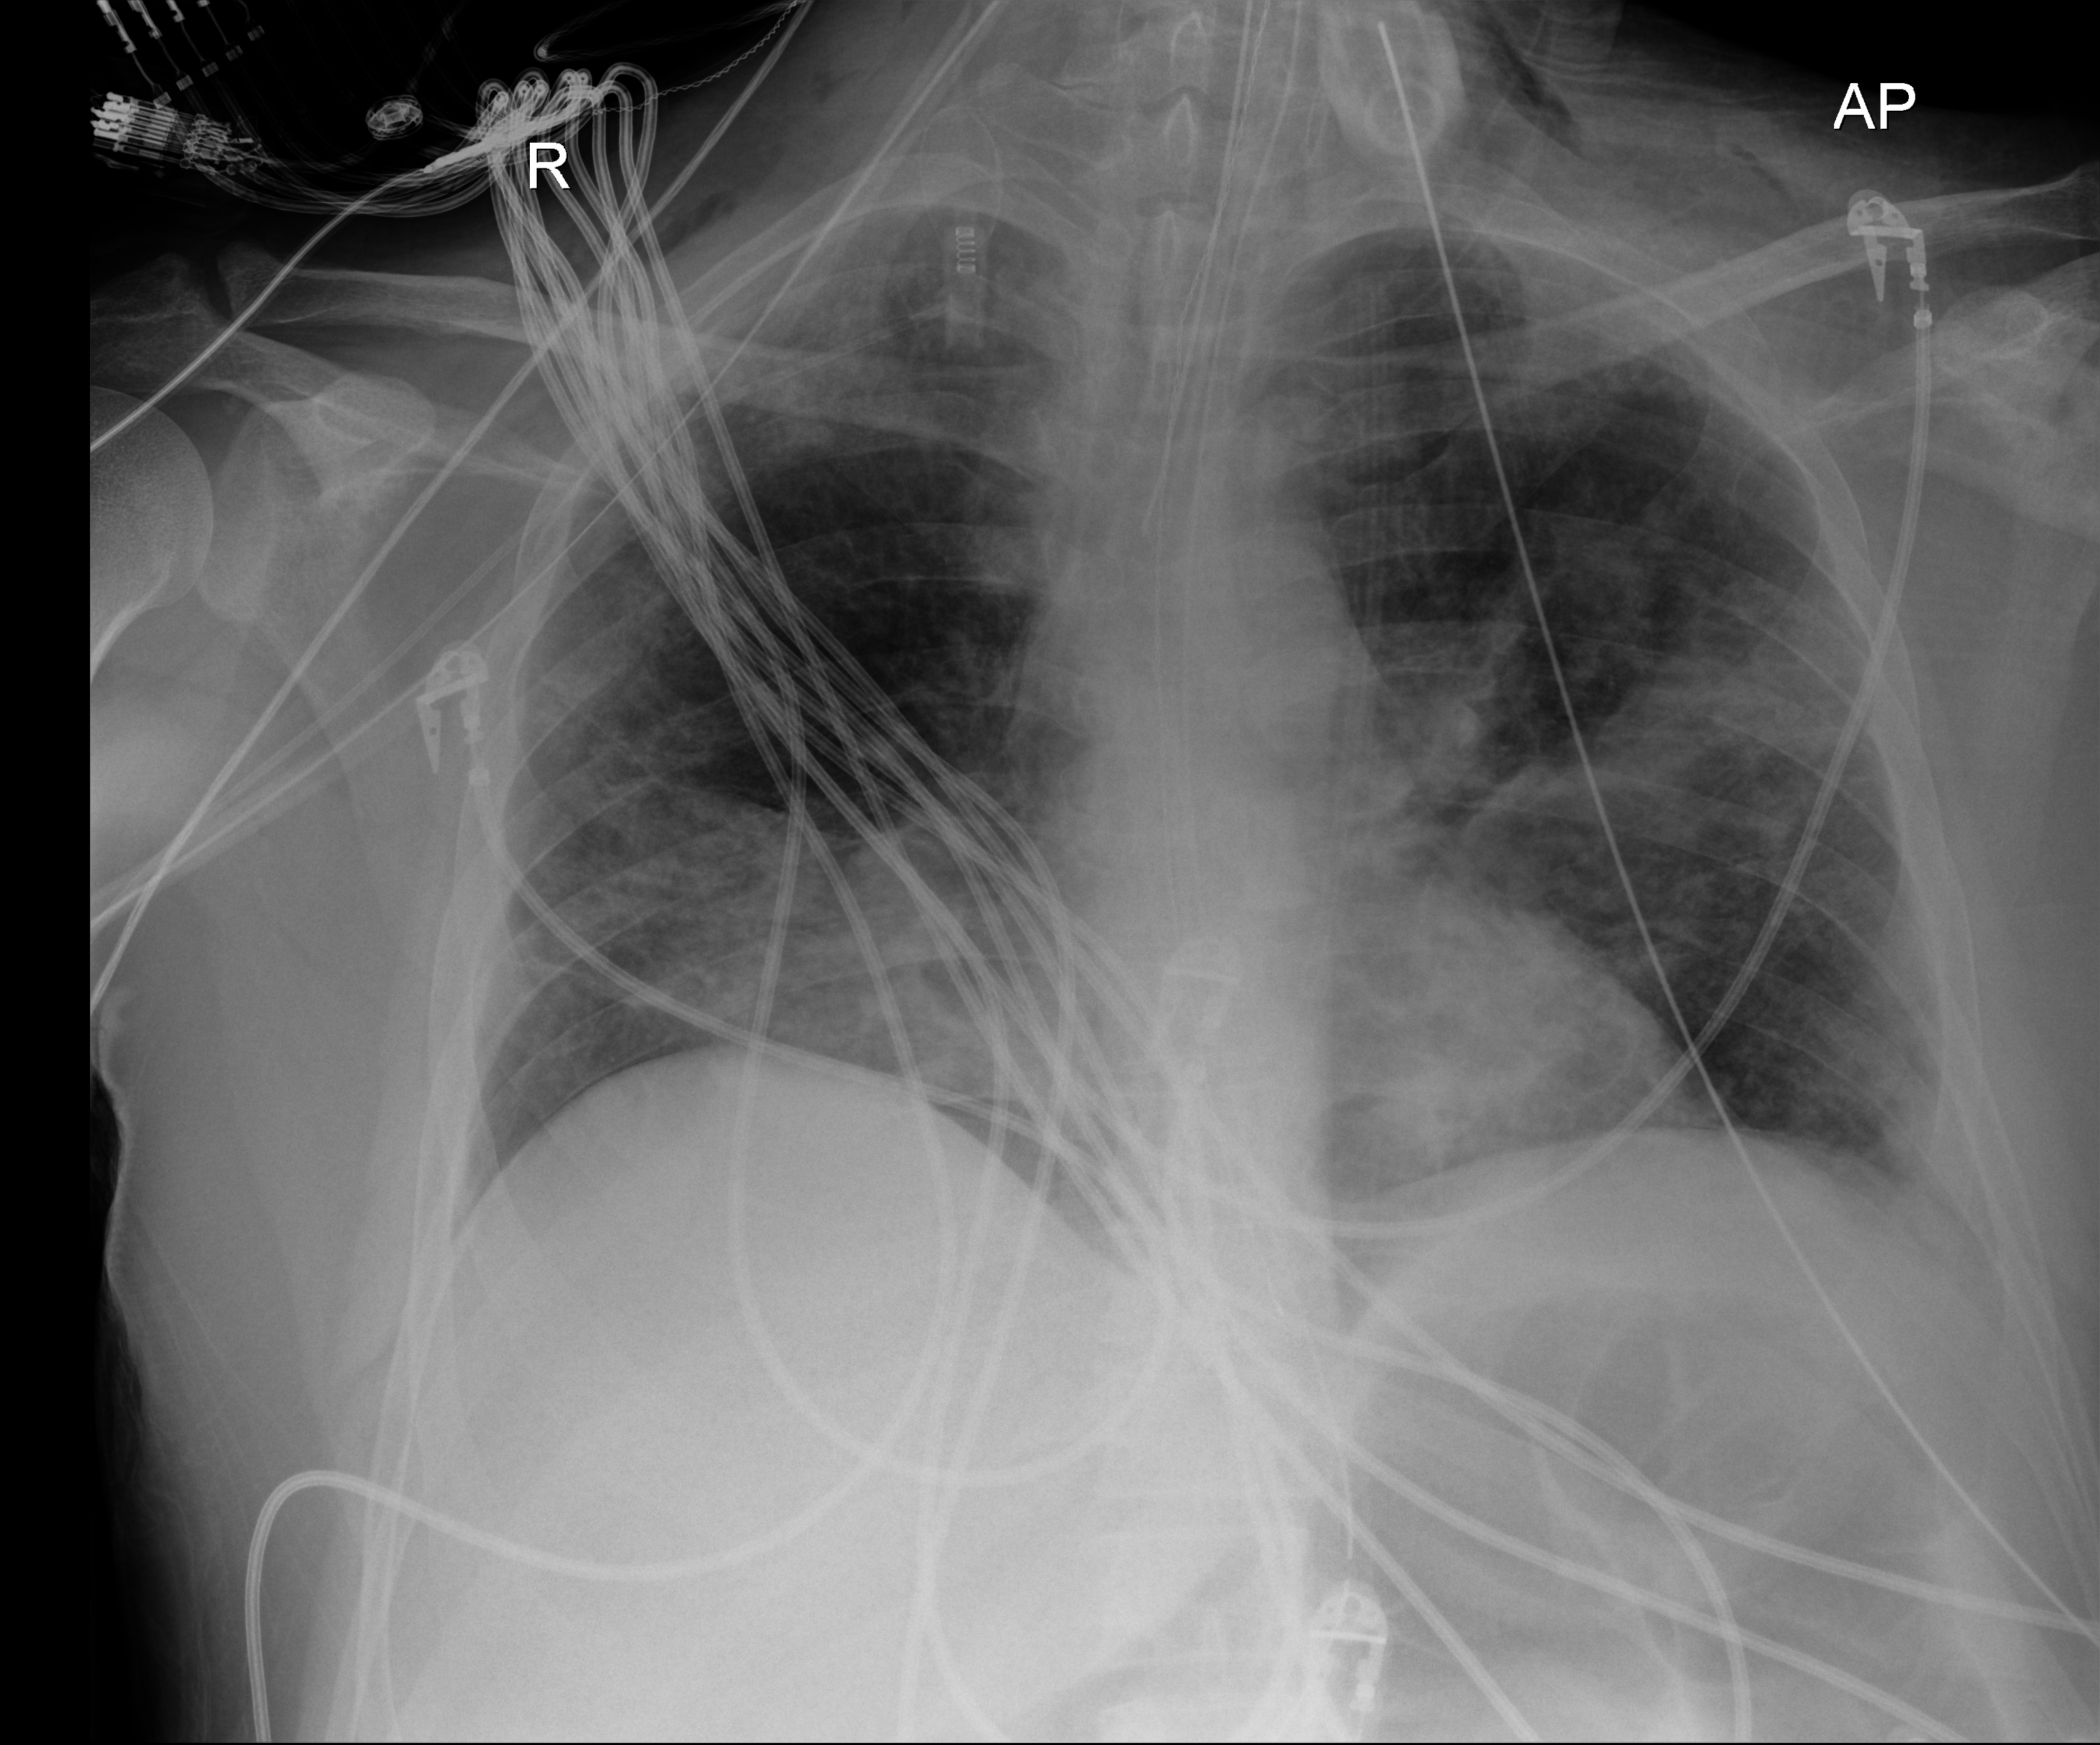
Chest radiograph. Adult patient hospitalised with COVID-19, age 18–59 years.
Hospital-stay facts (about this admission, not read from this image; timing relative to this image not recorded):
- admitted to intensive care during this hospital stay: yes
- length of hospital stay: 50 days